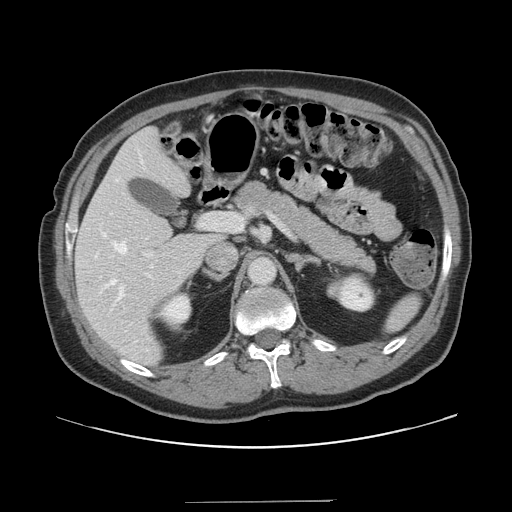
Contrast-enhanced abdominal CT, one axial slice; slice 86 of 151 in the series (ordered by position); 120 kVp; intravenous contrast given; soft-tissue window (W 400 / L 40 HU); 512 × 512 image matrix, field of view 399 × 399 mm. Male patient, age 63 years. From the clinical record (not read from this slice): diagnosis: colorectal cancer liver metastases, imaged before liver resection.
Structures marked on this image (outlined manually by an expert reader):
- hepatic veins: box from (x=102, y=160) to (x=143, y=332) px
- liver: (x=76, y=129)–(x=219, y=366)
- planned liver remnant (the part of the liver to remain after resection): (x=76, y=130)–(x=219, y=366)
- portal vein (with intrahepatic branches): (x=143, y=213)–(x=244, y=257)